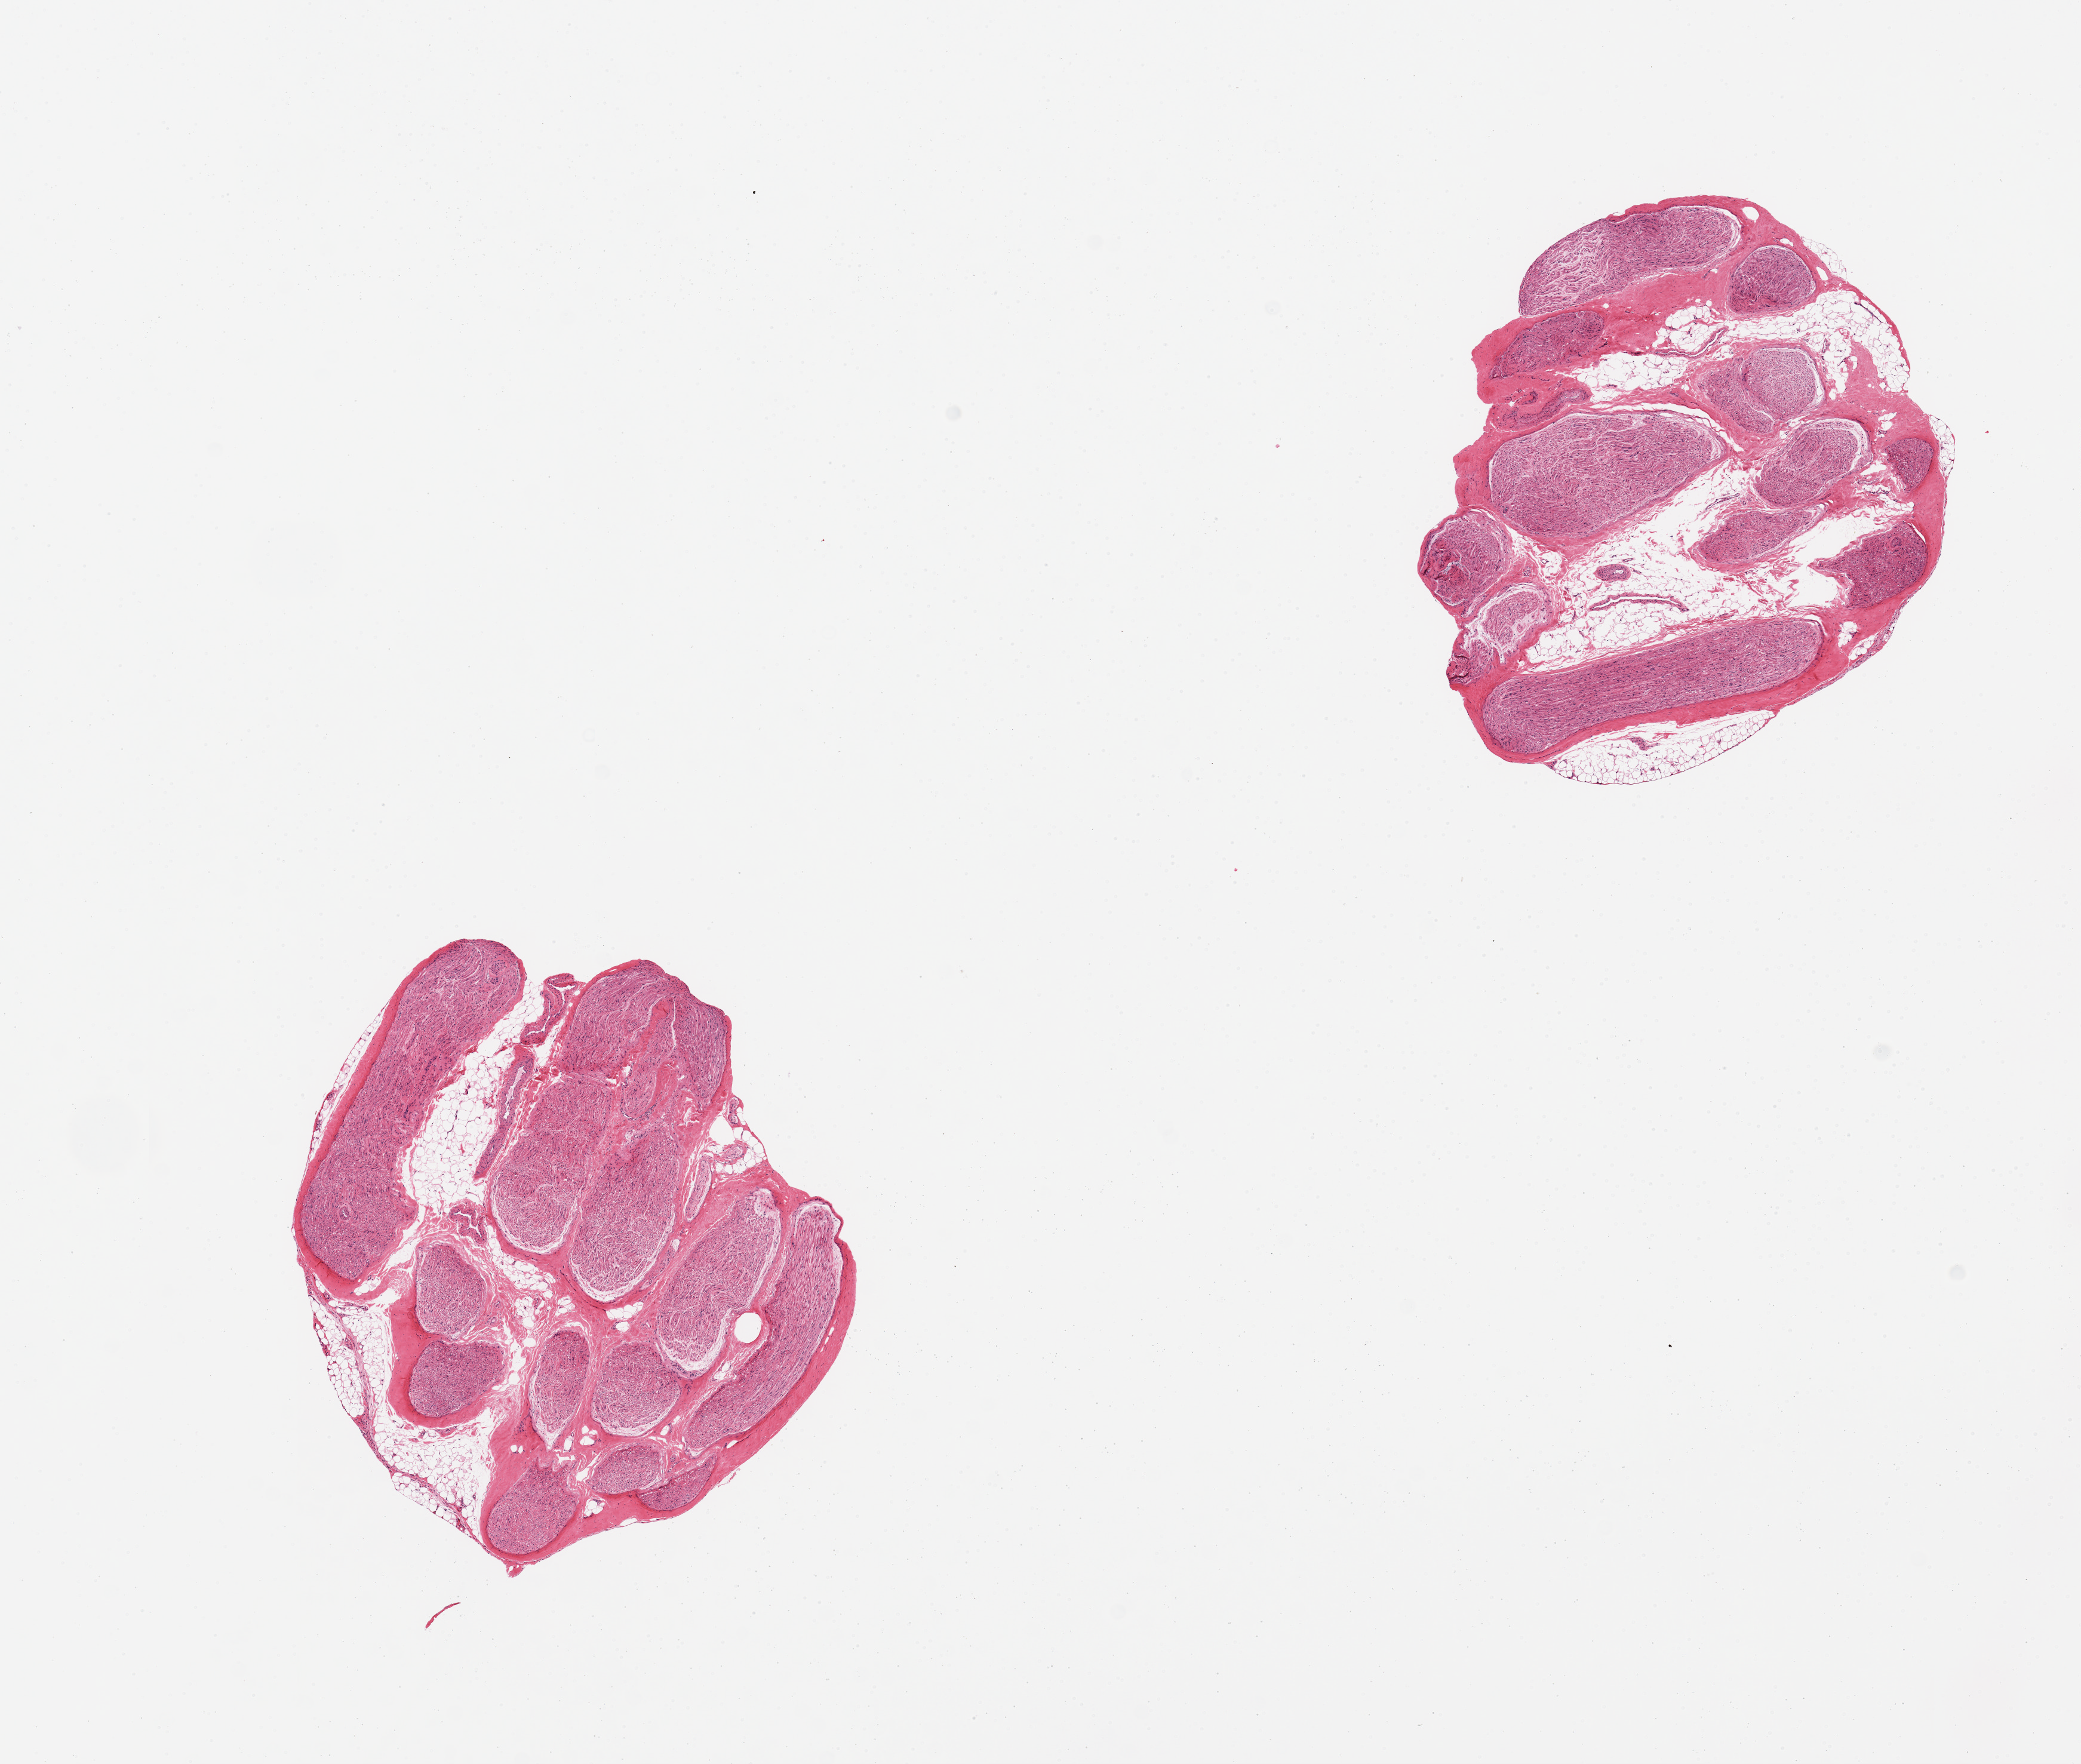
Haematoxylin and eosin whole-slide image, brightfield — whole scanned area (about 13.8 x 11.7 mm) shown as a low-resolution overview. PAXgene-fixed paraffin-embedded (PFPE) section. Section of tibial nerve (target tissue). Donor tissue sample. Donor: male.
Pathologist's review note for this sample: 2 pieces, includes 10-20% predominantly internal adipose tissue.